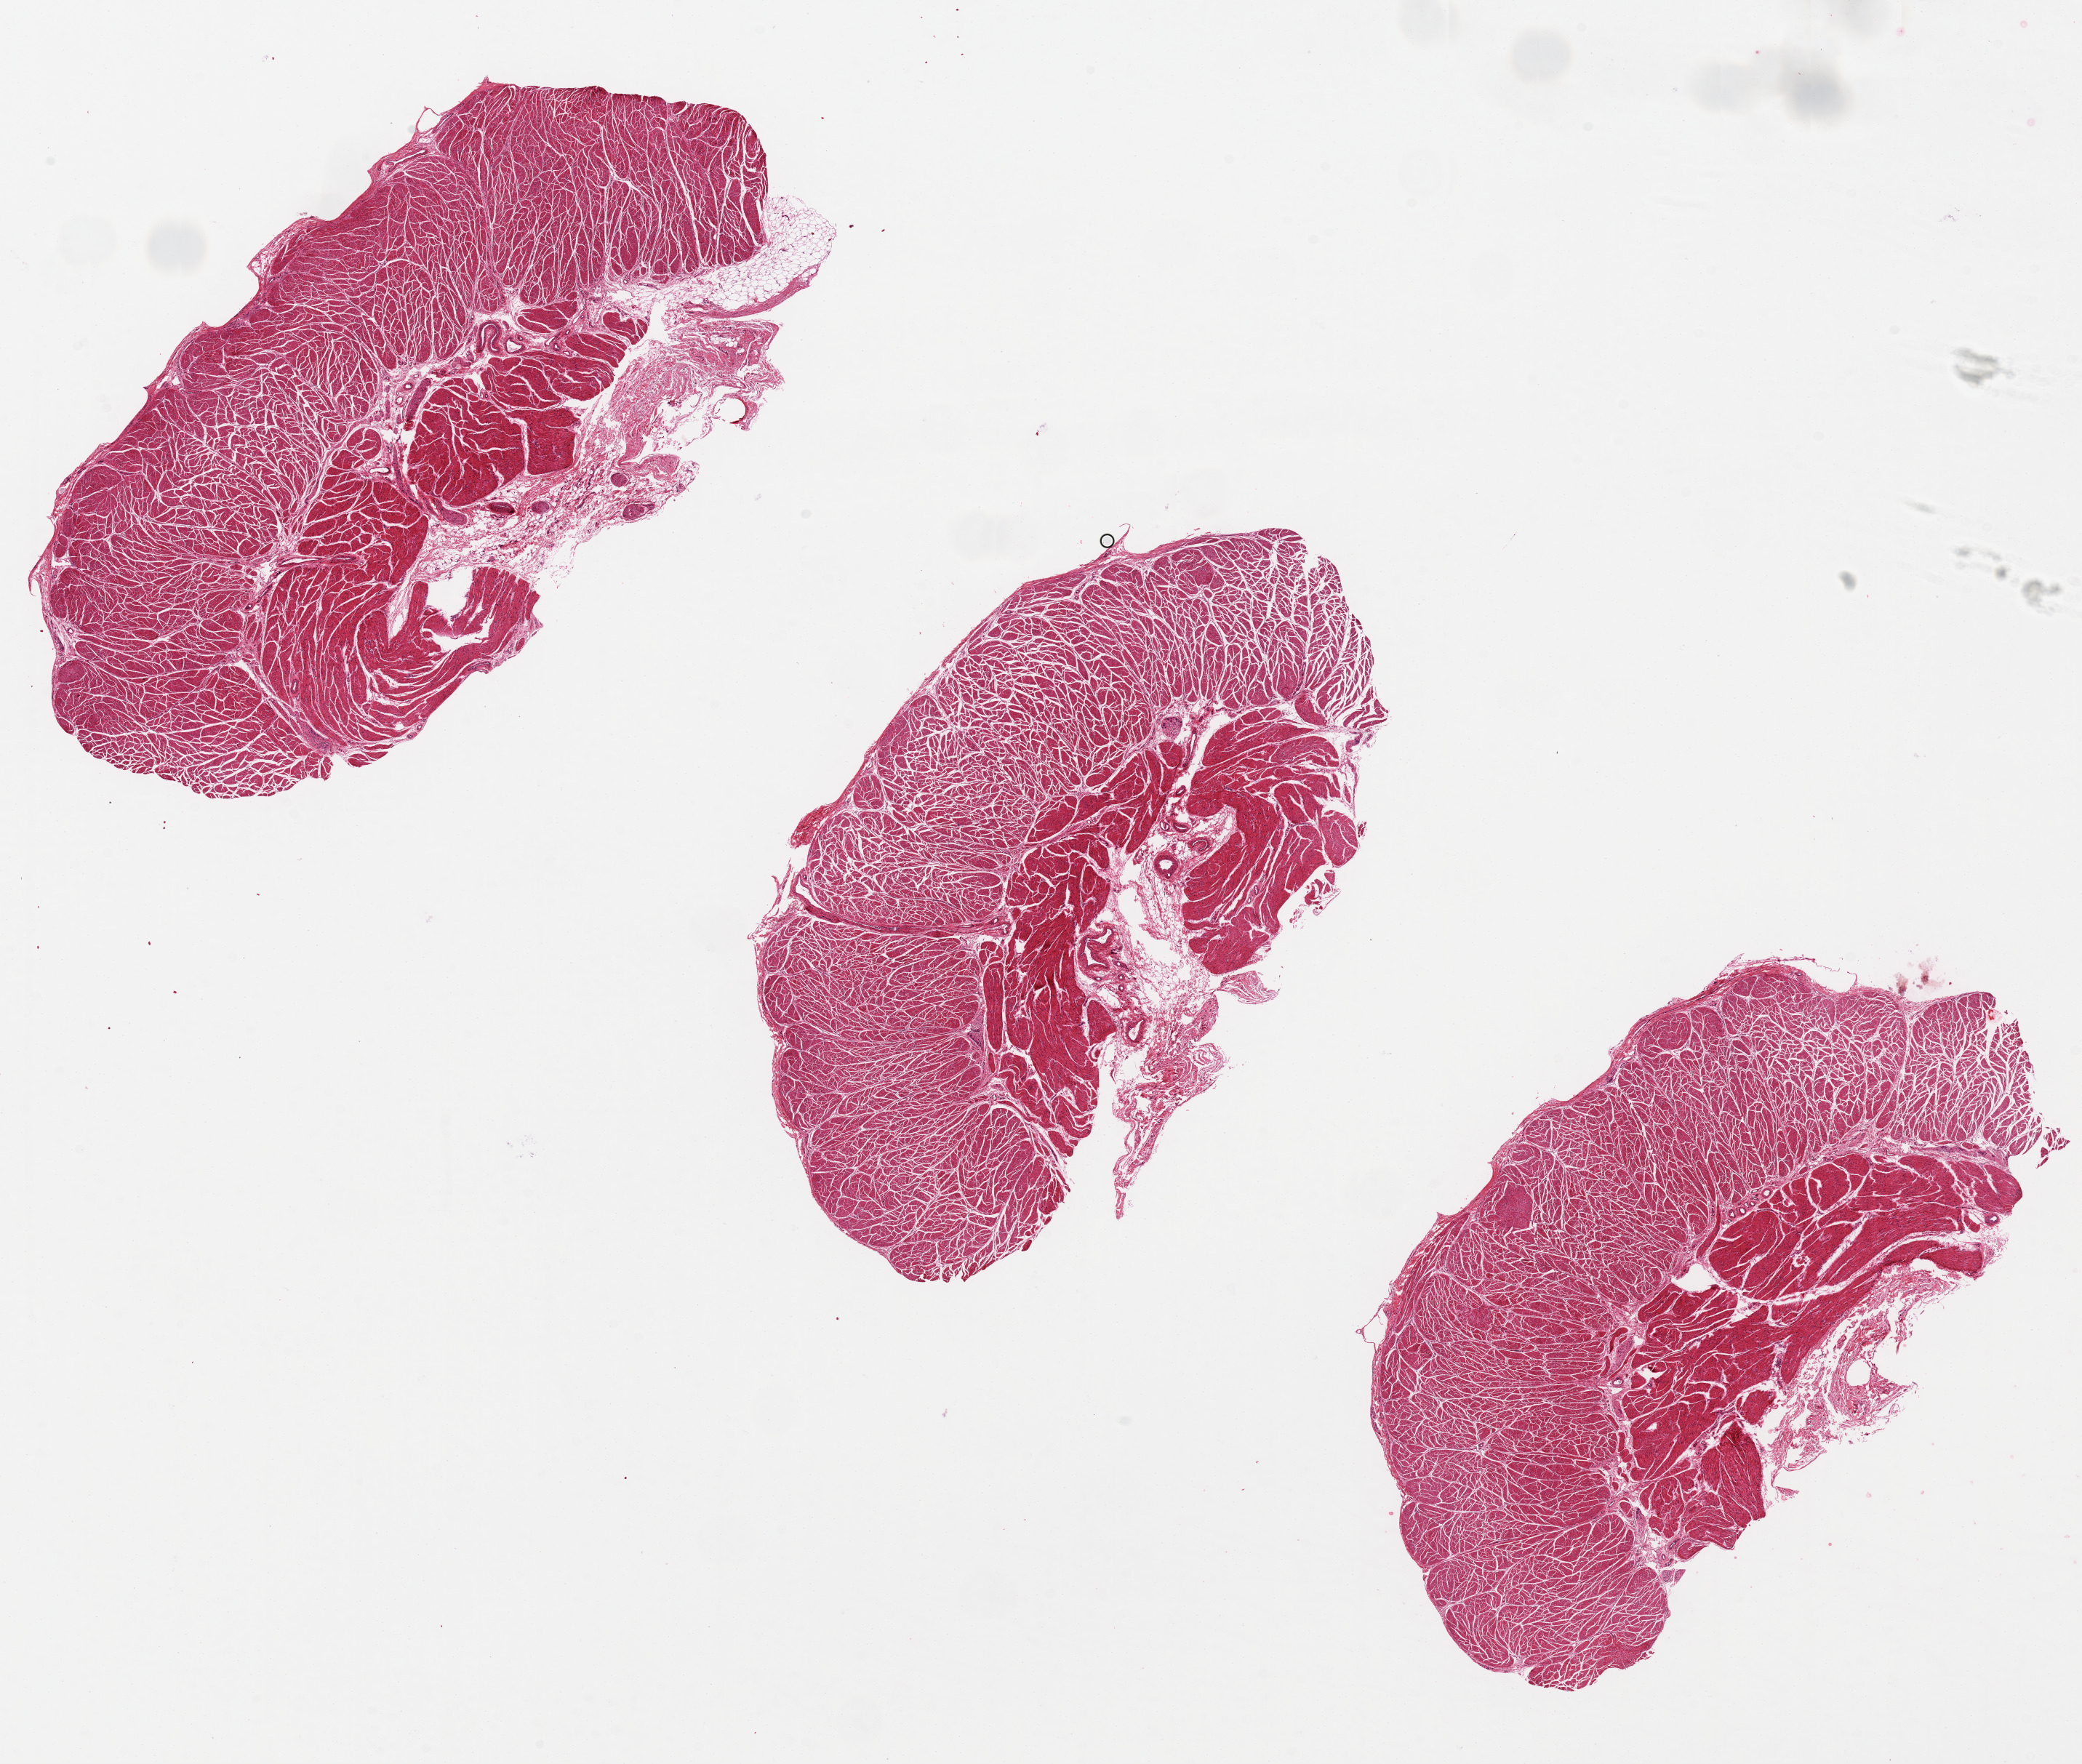
Whole-slide image, hematoxylin and eosin (H&E) stain — a low-resolution overview of the entire scanned area, about 22.6 x 19.2 mm (slide scanned at 20x). PAXgene-fixed paraffin-embedded (PFPE) section. Section of esophageal muscle (target tissue). Tissue donor sample. Donor sex: male.
Review note (as recorded): Cassette pressure marks. 9.8x5mm.